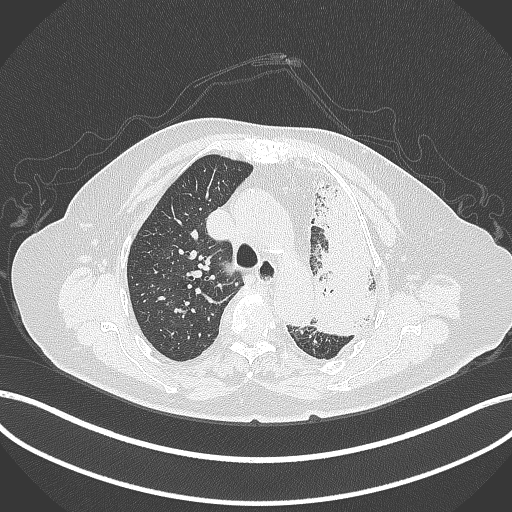
Chest CT, one axial slice; slice 287 of 399 in the series (ordered by position); reconstruction kernel B70f; 120 kVp; lung window (W 1500 / L -600 HU); 1 mm slice thickness; 512 × 512 image matrix. Female patient, age 75 years. From the clinical record (not read from this slice): clinical TNM (as recorded): T3 N3 M1.
Outlined on this slice (bounding box drawn by a radiologist):
- lung tumour (recorded histology: adenocarcinoma): box from (x=305, y=179) to (x=387, y=339) px